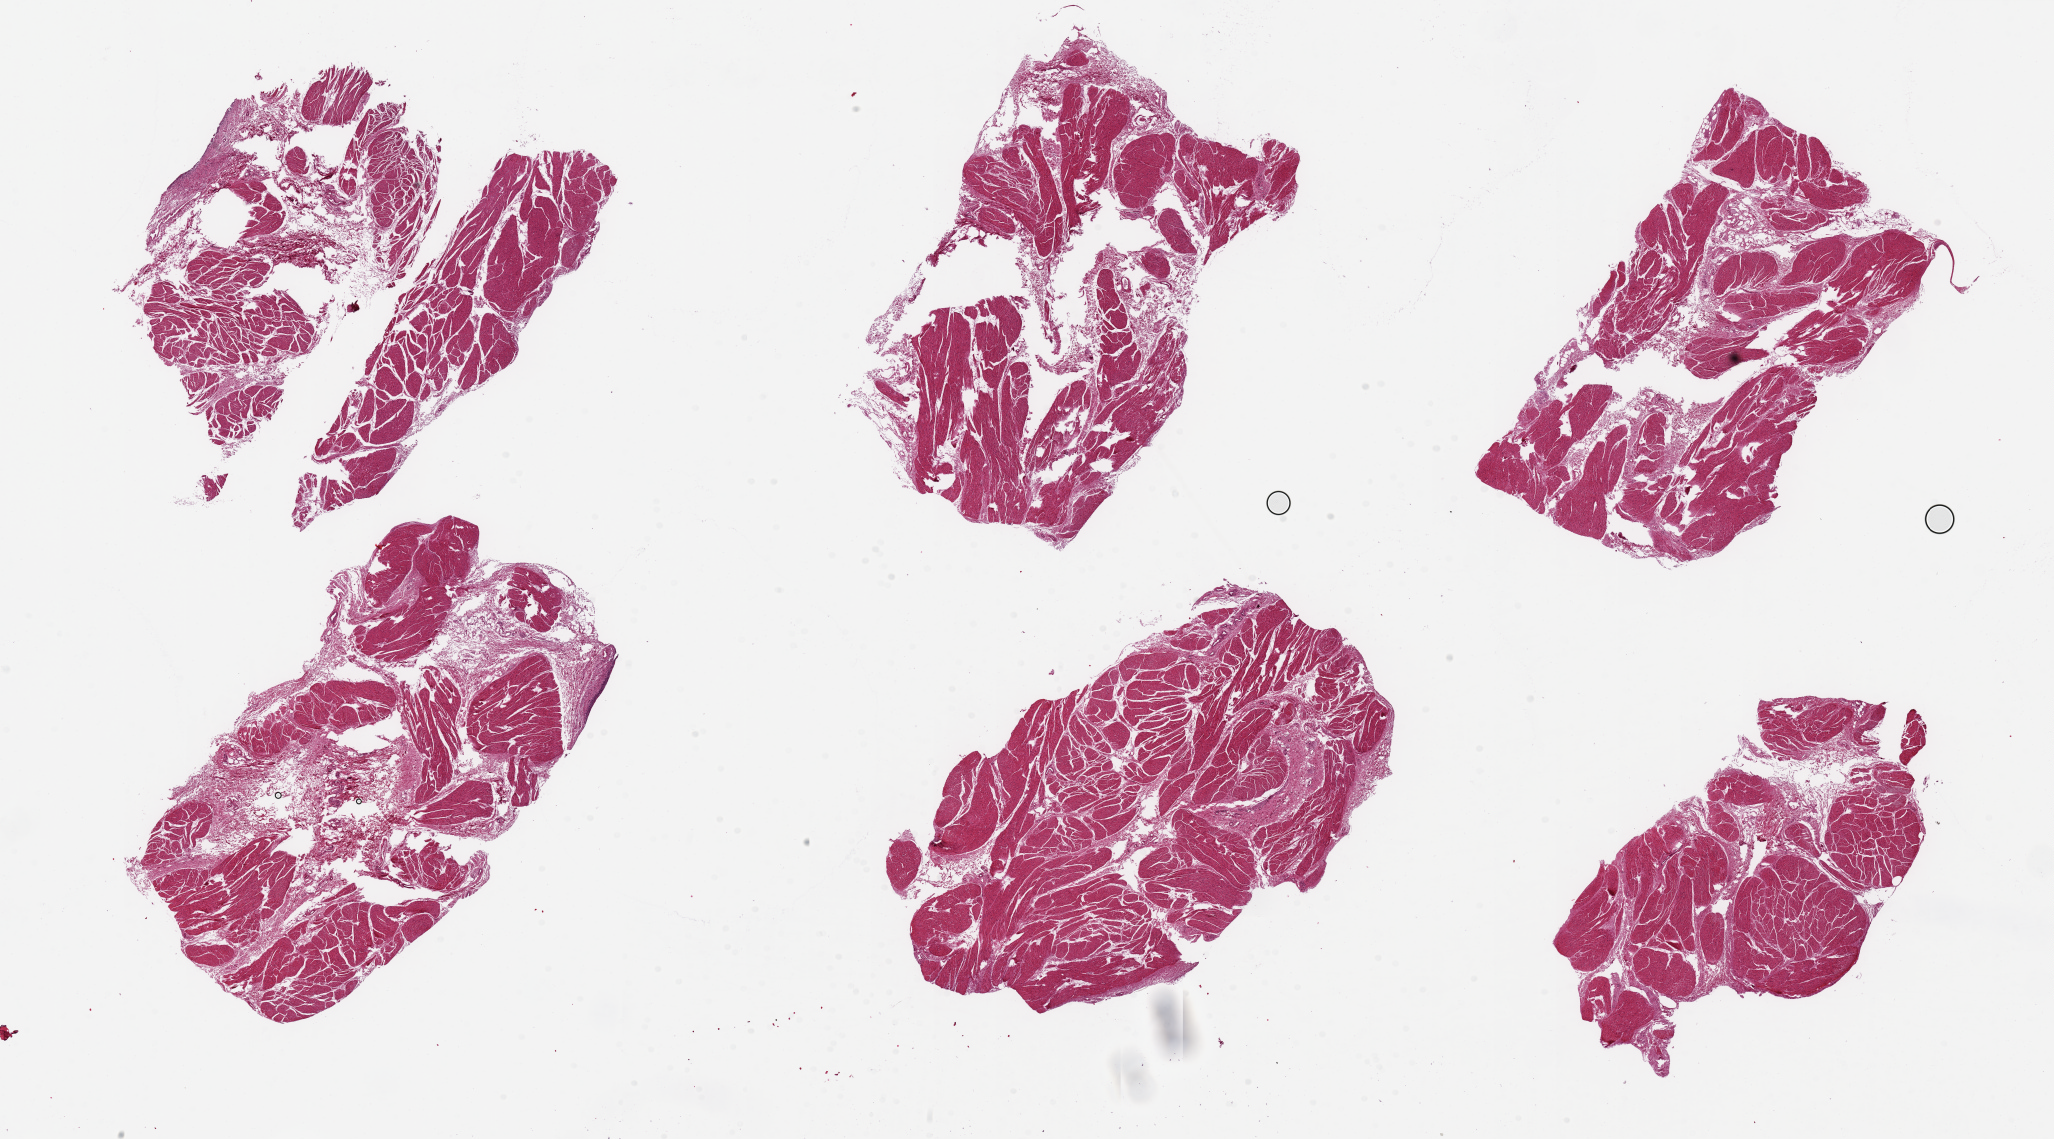
Whole-slide image, H&E stain — shown as a low-resolution overview of the whole scanned area (about 32.5 x 18.0 mm), PAXgene-fixed, paraffin-embedded tissue, target tissue: urinary bladder, tissue donor sample. Male donor.
Reviewer comment on this tissue sample: 6 pieces up to 8x5mm; little epithelium, what is present is largely sloughed; lots of tissue fractures.